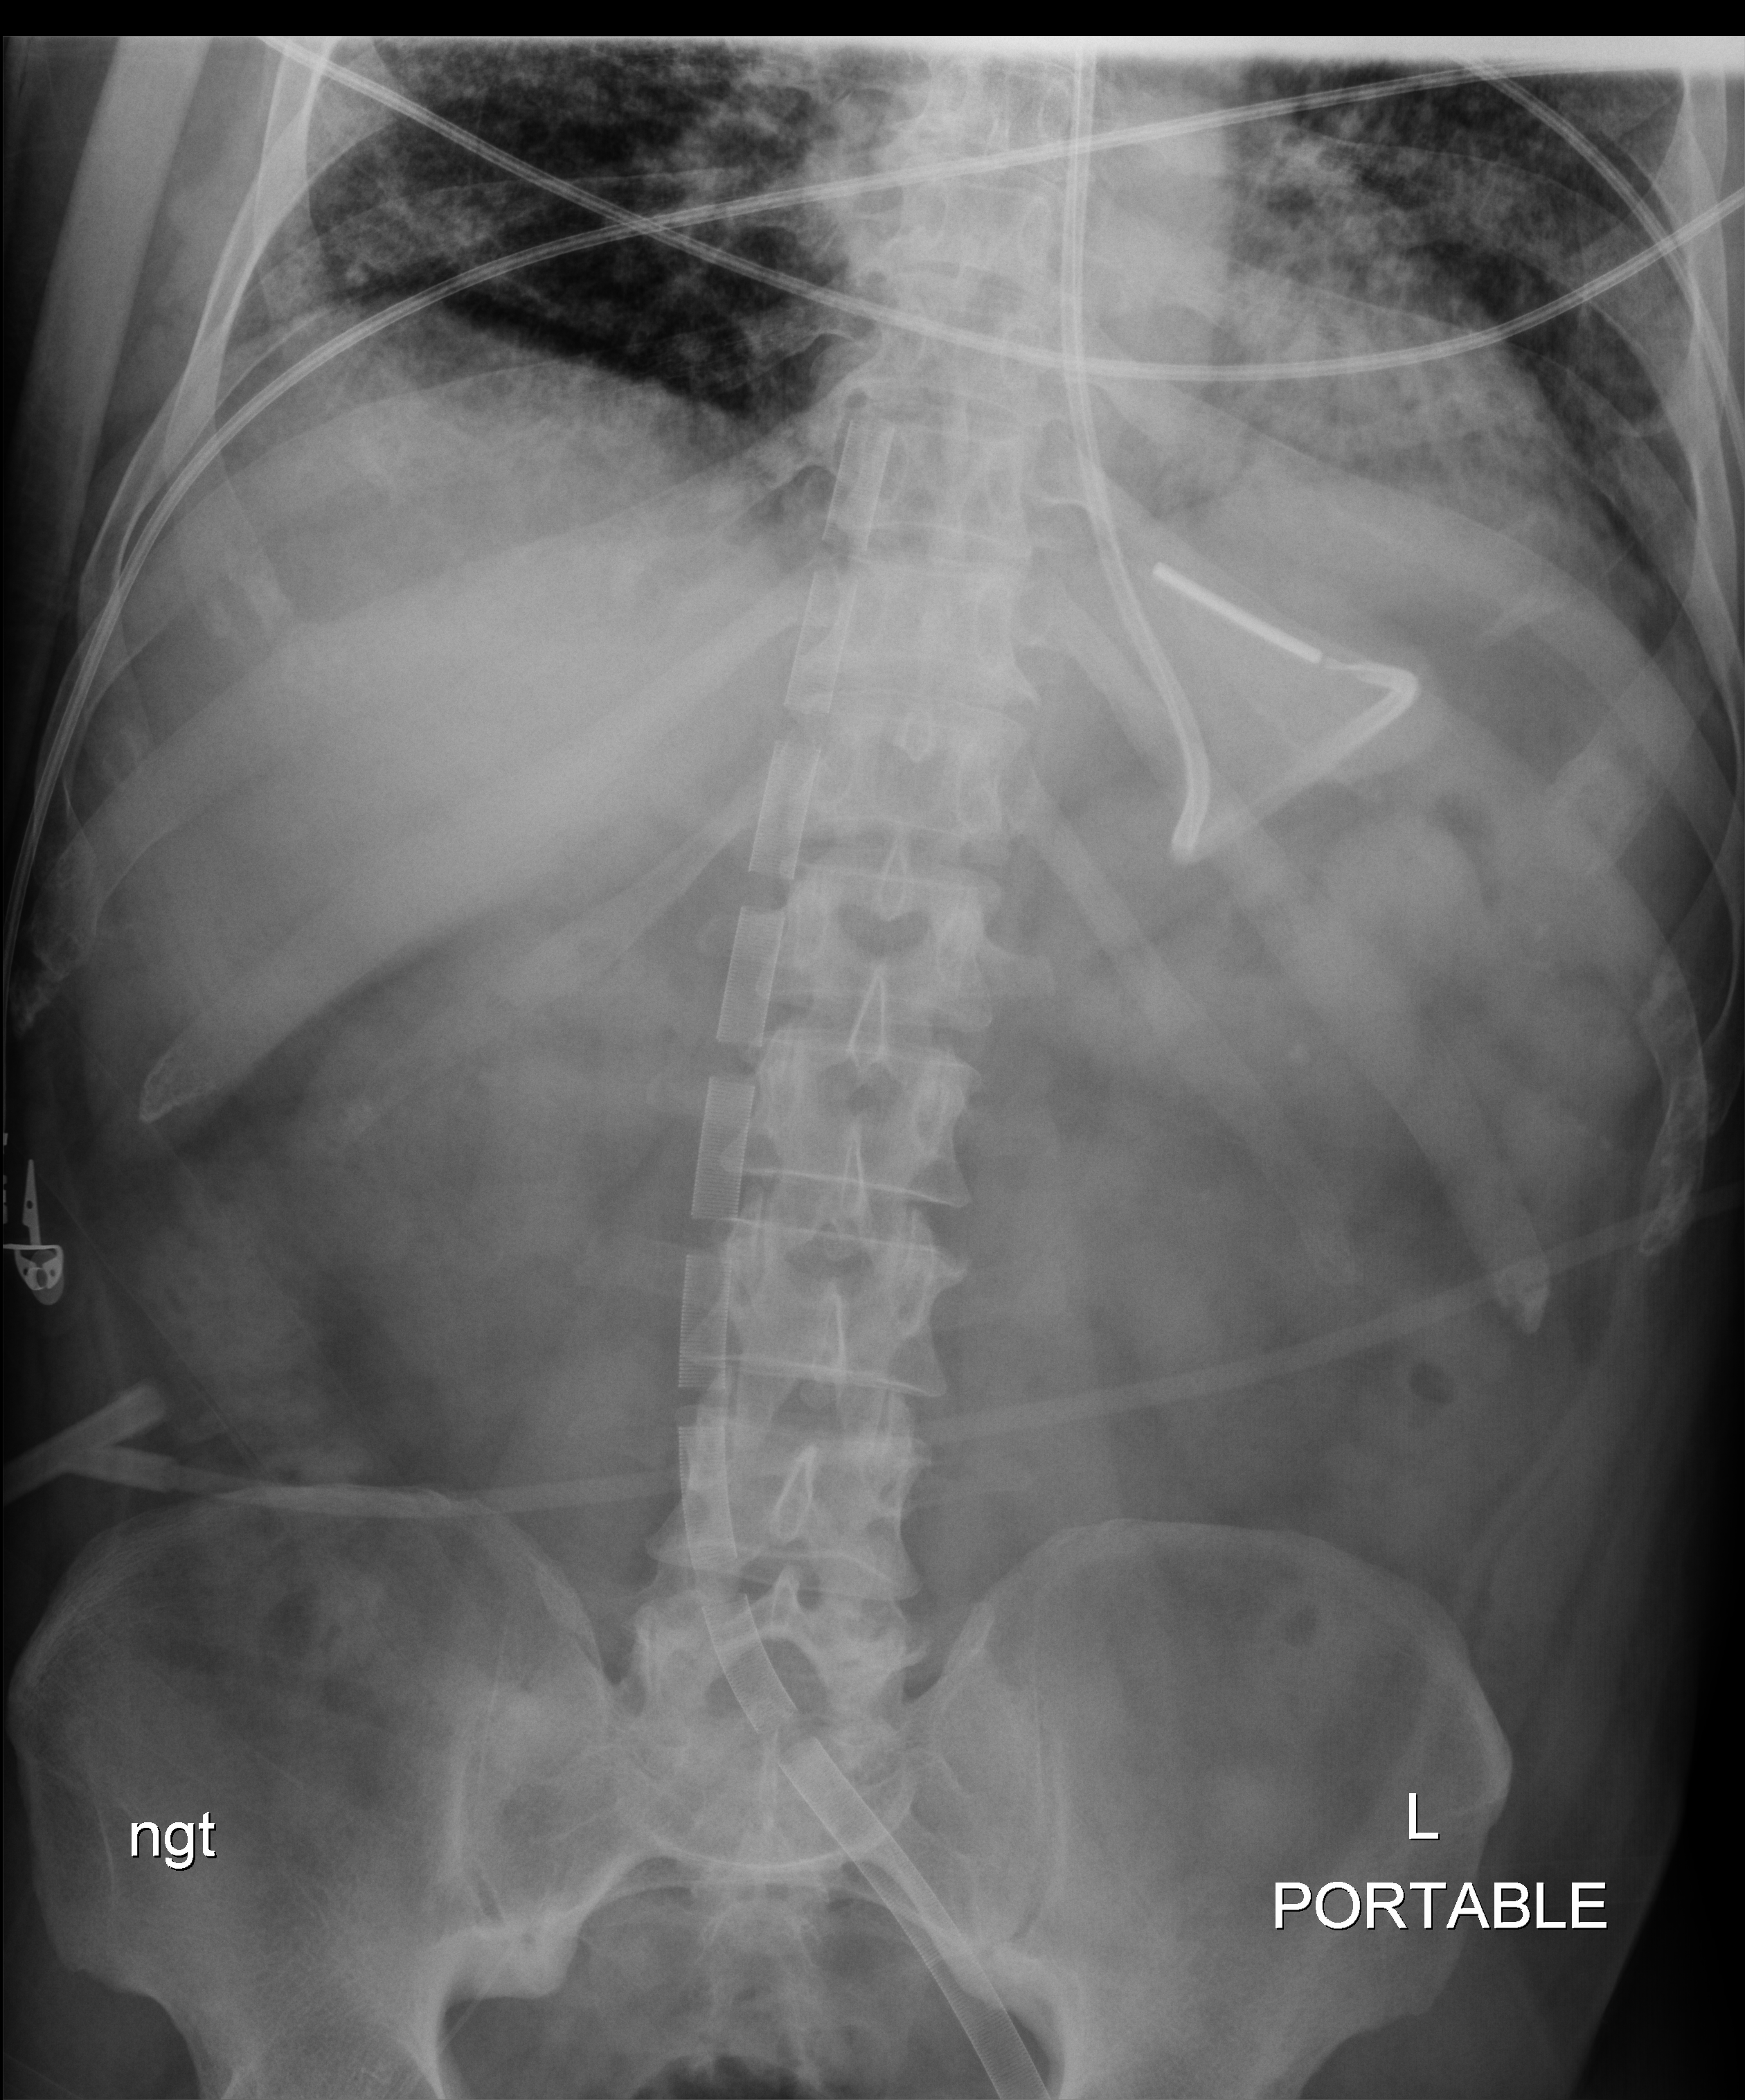
Abdomen X-ray (portable); anteroposterior (AP) projection. Patient hospitalised with COVID-19; male, aged 18–59 years.
From the hospital-stay record, not from the radiograph (when in the stay this image was taken is not recorded): COPD (admission record): no; mechanically ventilated during this hospital stay: yes; admitted to intensive care during this hospital stay: yes.